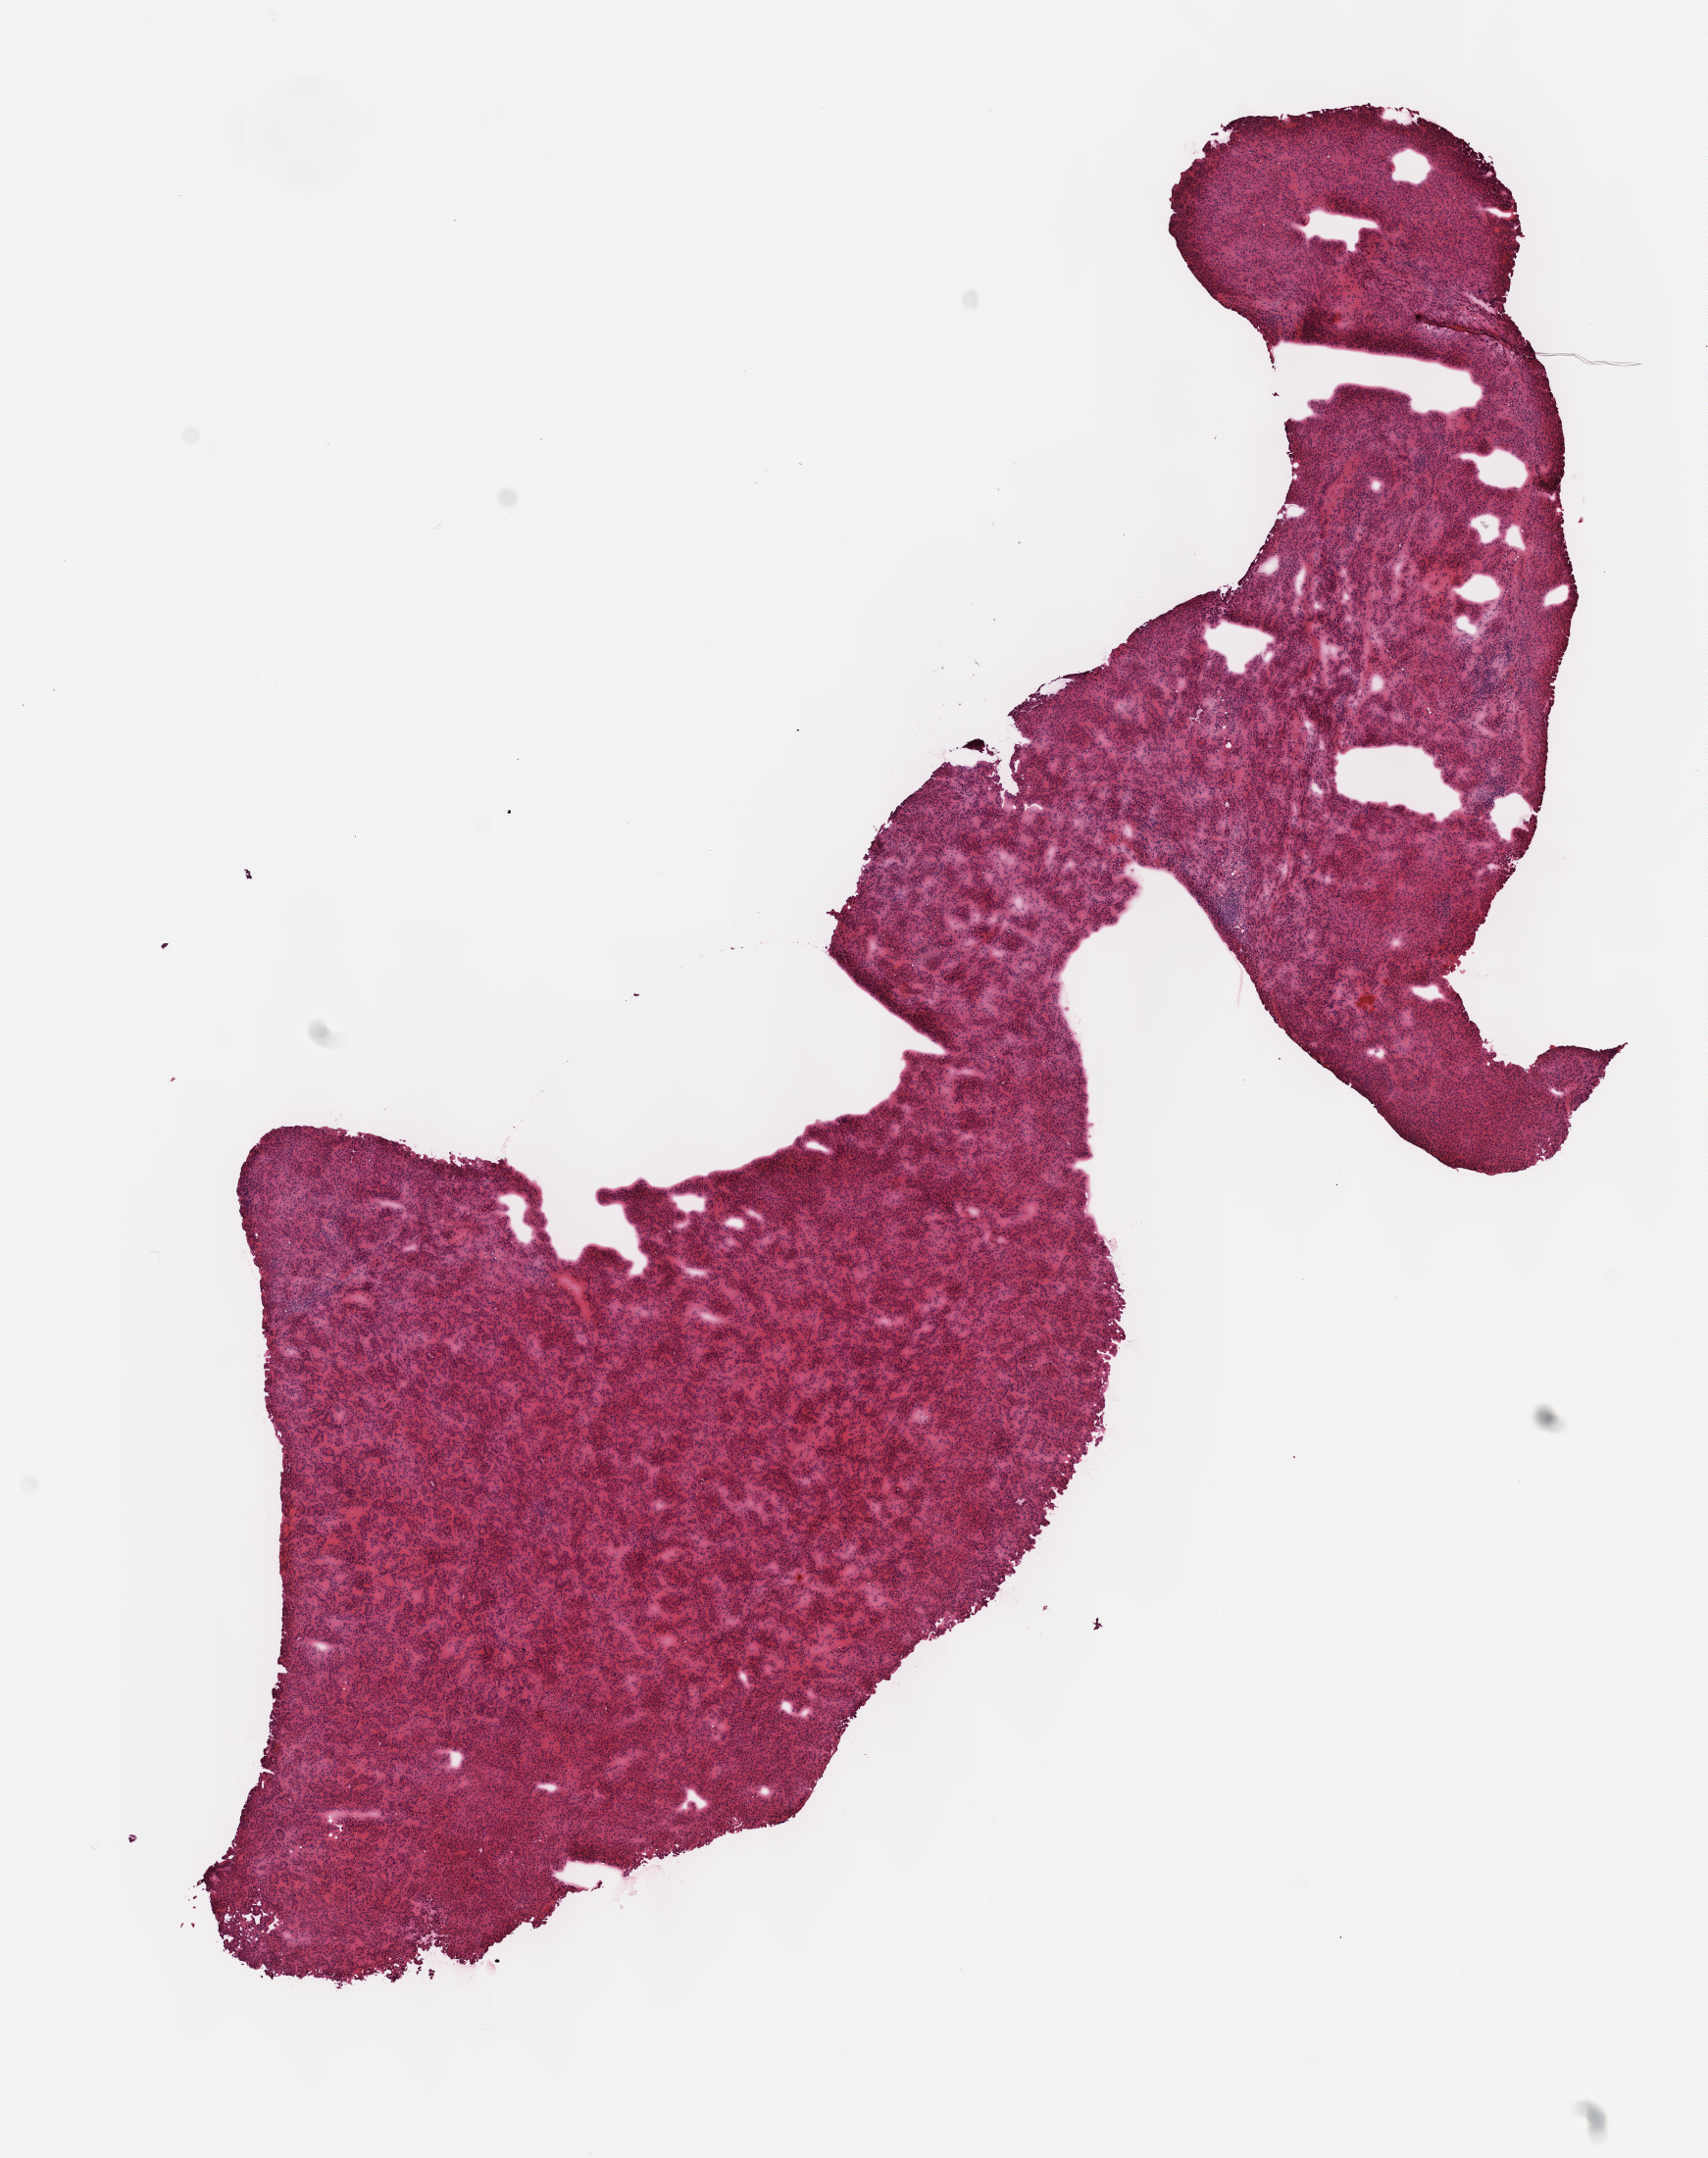
Whole-slide histology image, Hematoxylin and eosin (H&E) stained — whole scanned area (about 7.0 x 8.9 mm, from a 40x scan) shown as a low-resolution overview. Frozen section. Primary tumour sample from the liver. Female patient; age at initial diagnosis 49 years. Histologic grade: G1 (well differentiated). Slide review estimates, as recorded: tumour cells 100%, tumour nuclei 80%, normal cells 0%, stromal cells 0%, necrosis 0%. Infiltration values recorded for this section: lymphocyte infiltration 2%, monocyte infiltration 0%, neutrophil infiltration 0%.
* AJCC pathologic stage: I
* histologic diagnosis: Hepatocellular carcinoma, NOS